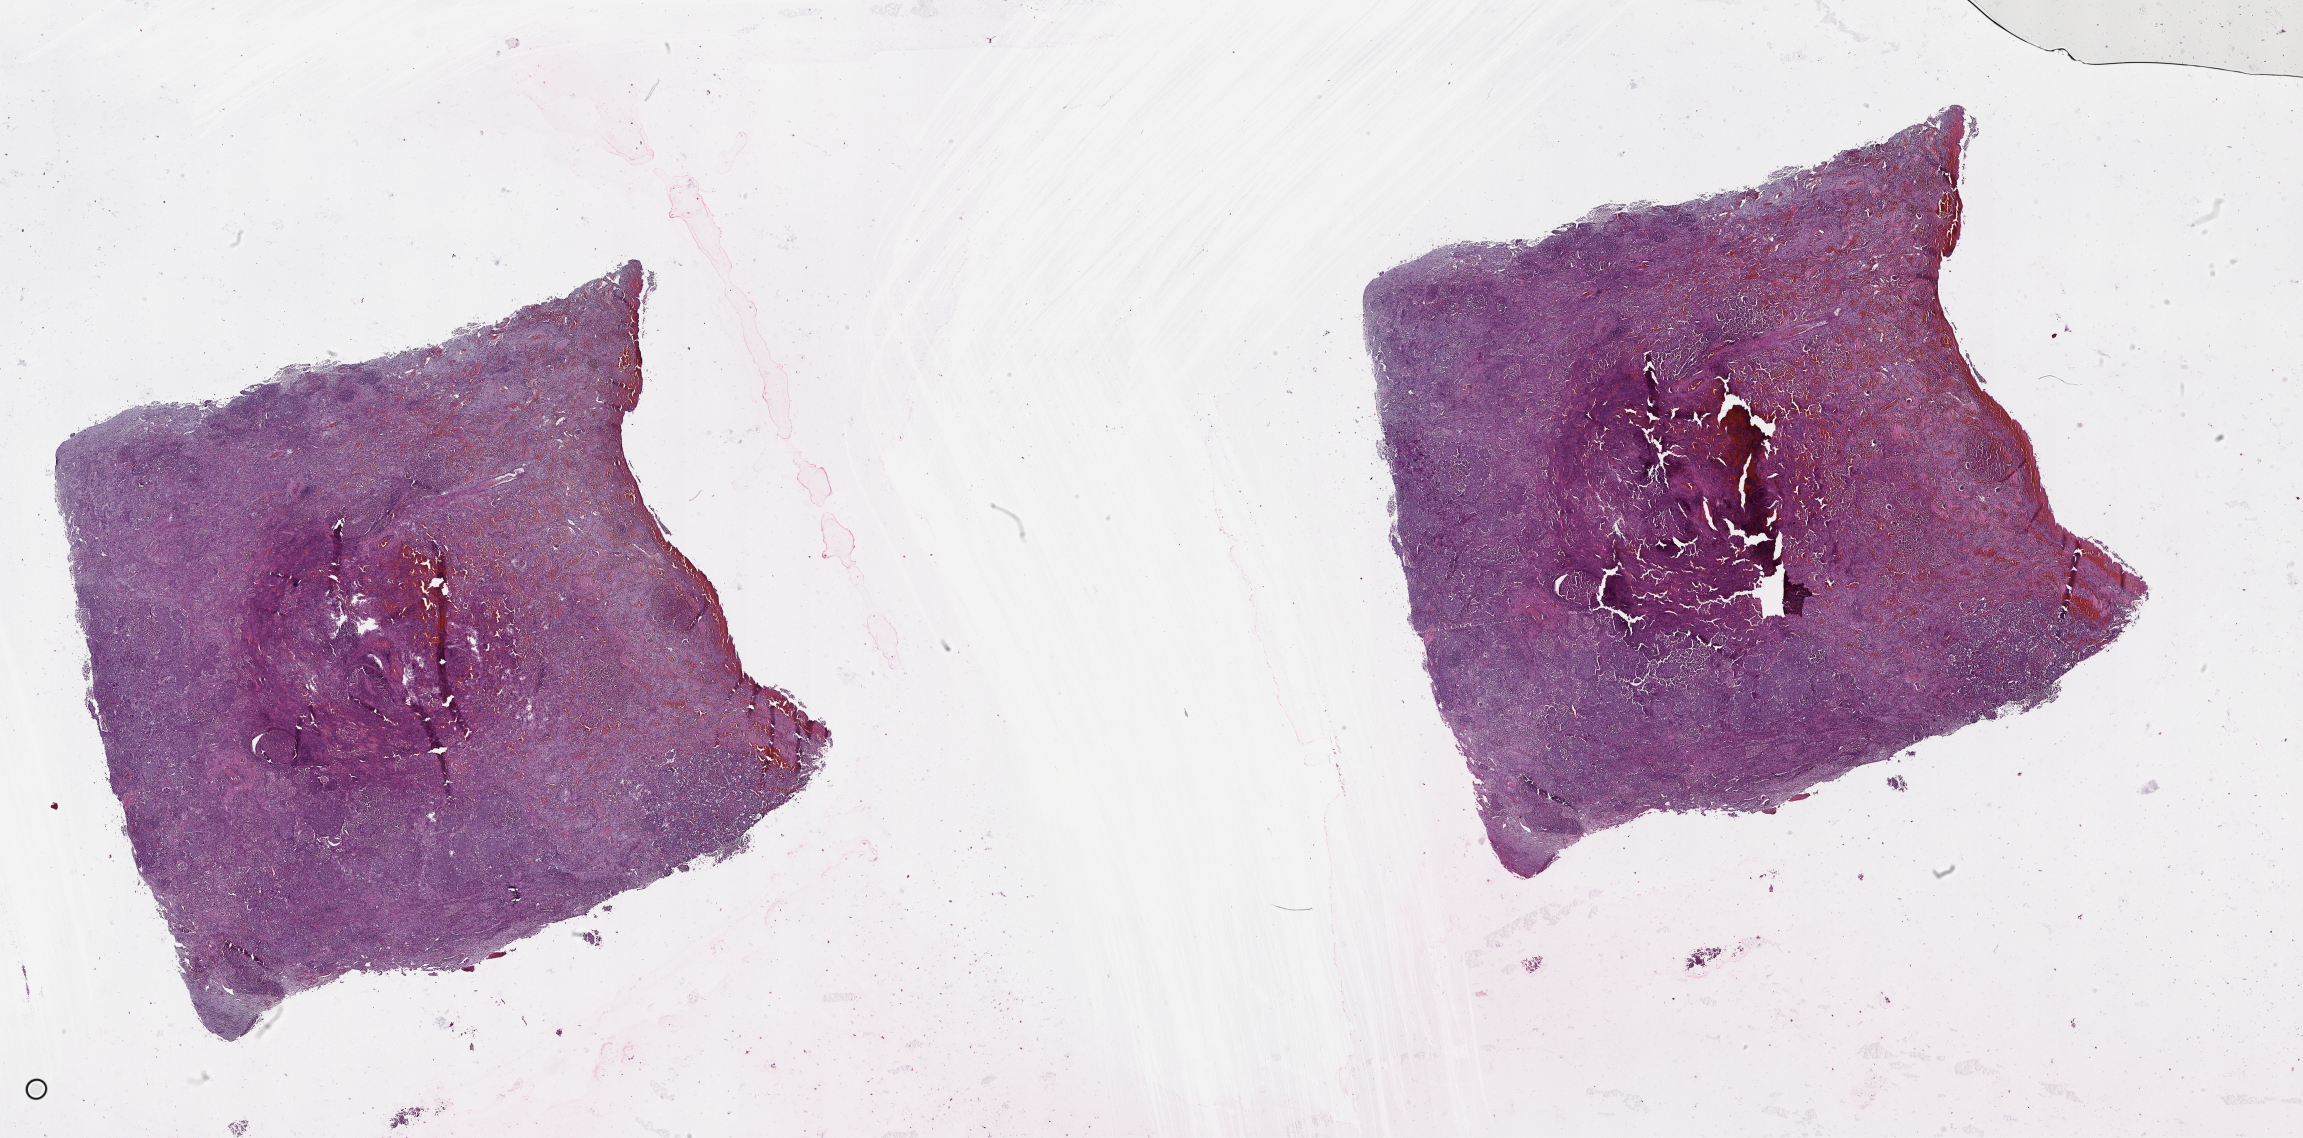
H&E whole-slide image — shown as a low-resolution overview of the whole scanned area (about 37.1 x 18.3 mm, acquisition: 20x scan); tumour tissue sample, lung. 67-year-old male patient.
Patient diagnosis (cohort enrolment): squamous cell carcinoma (lung).